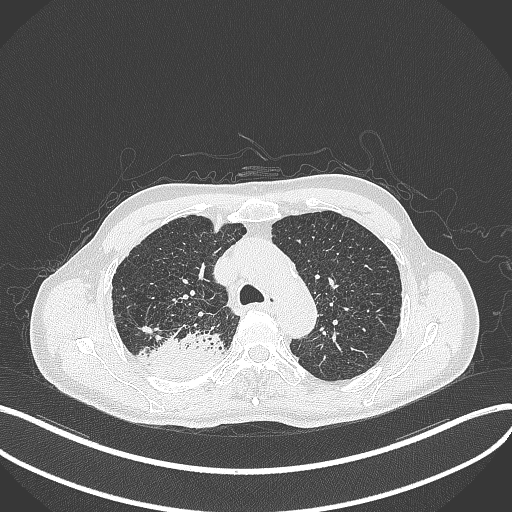
Chest CT, one axial slice. Slice 328 of 428 in the series (ordered by position). 120 kVp. Lung window (W 1500 / L -600 HU). 1 mm slice thickness. 512 × 512 image matrix, field of view 400 × 400 mm. Patient: male, 79 years. From the clinical record (not read from this slice): clinical TNM (as recorded): T3 N0 M0.
Structures marked on this image (rectangle marked by the reading radiologist):
- lung tumour (recorded histology: adenocarcinoma): bounding box (x1, y1, x2, y2) in pixels: (147, 327, 225, 379)